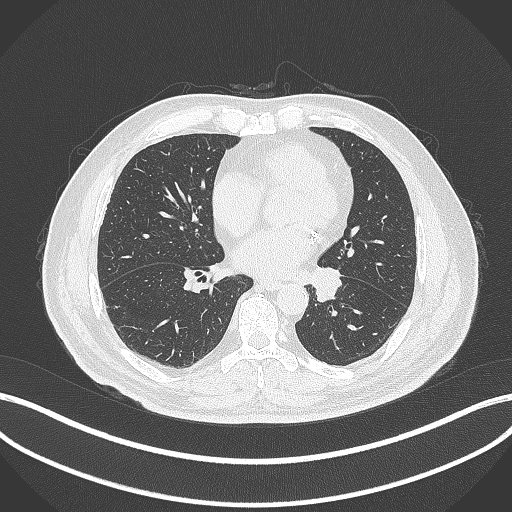
Chest CT, one axial slice. Slice 122 of 312 in the series (ordered by position). Reconstruction kernel B70f. Lung window (W 1500 / L -600 HU). 1 mm slice thickness. 512 × 512 image matrix, field of view 400 × 400 mm. Patient: male, 71 years. From the clinical record (not read from this slice): clinical TNM (as recorded): T1b N0 M0.
Annotated regions visible in this slice (rectangle marked by the reading radiologist):
- lung tumour (recorded histology: squamous cell carcinoma): bounding box (x1, y1, x2, y2) in pixels: (308, 264, 348, 303)